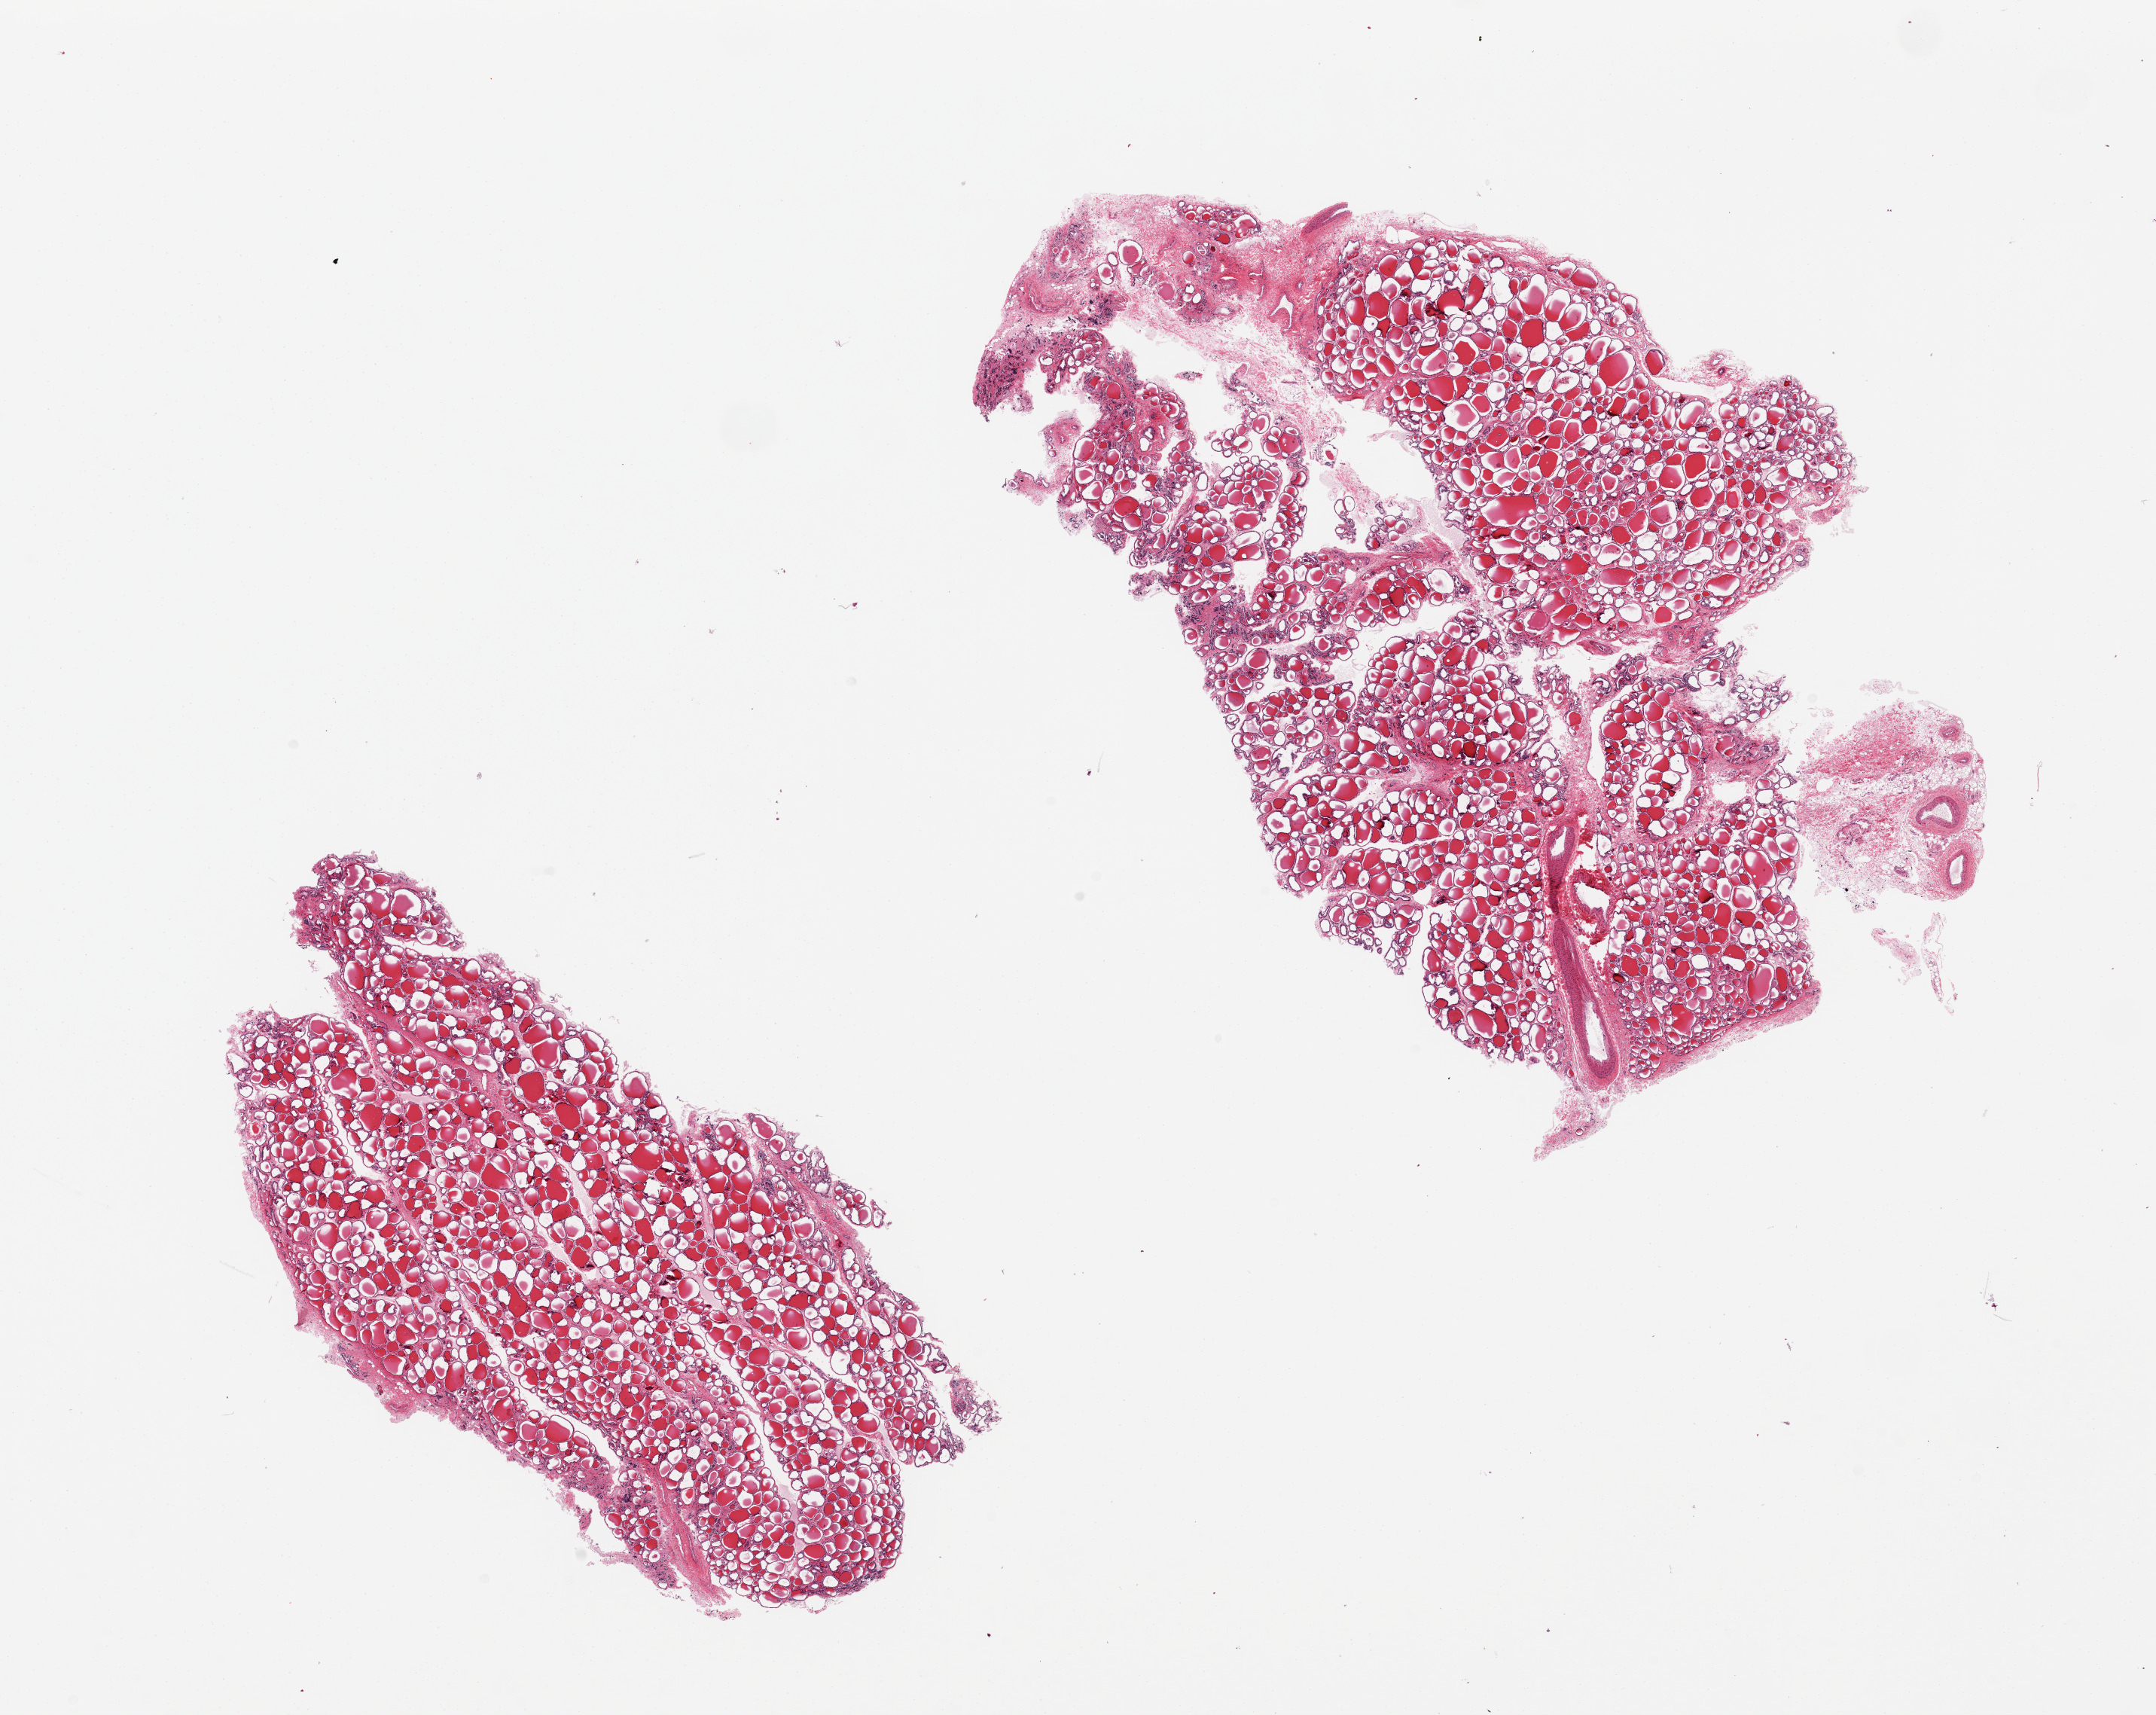
Whole-slide image, H&E stain, low-resolution overview of the scanned area, about 22.6 x 18.0 mm (from a 20x scan), PAXgene-fixed paraffin-embedded (PFPE) section, target tissue: thyroid, donor tissue sample. Donor sex: female.
* pathologist's review note for this sample: 2 pieces, larger piece includes ~10% fibrofatty tissue